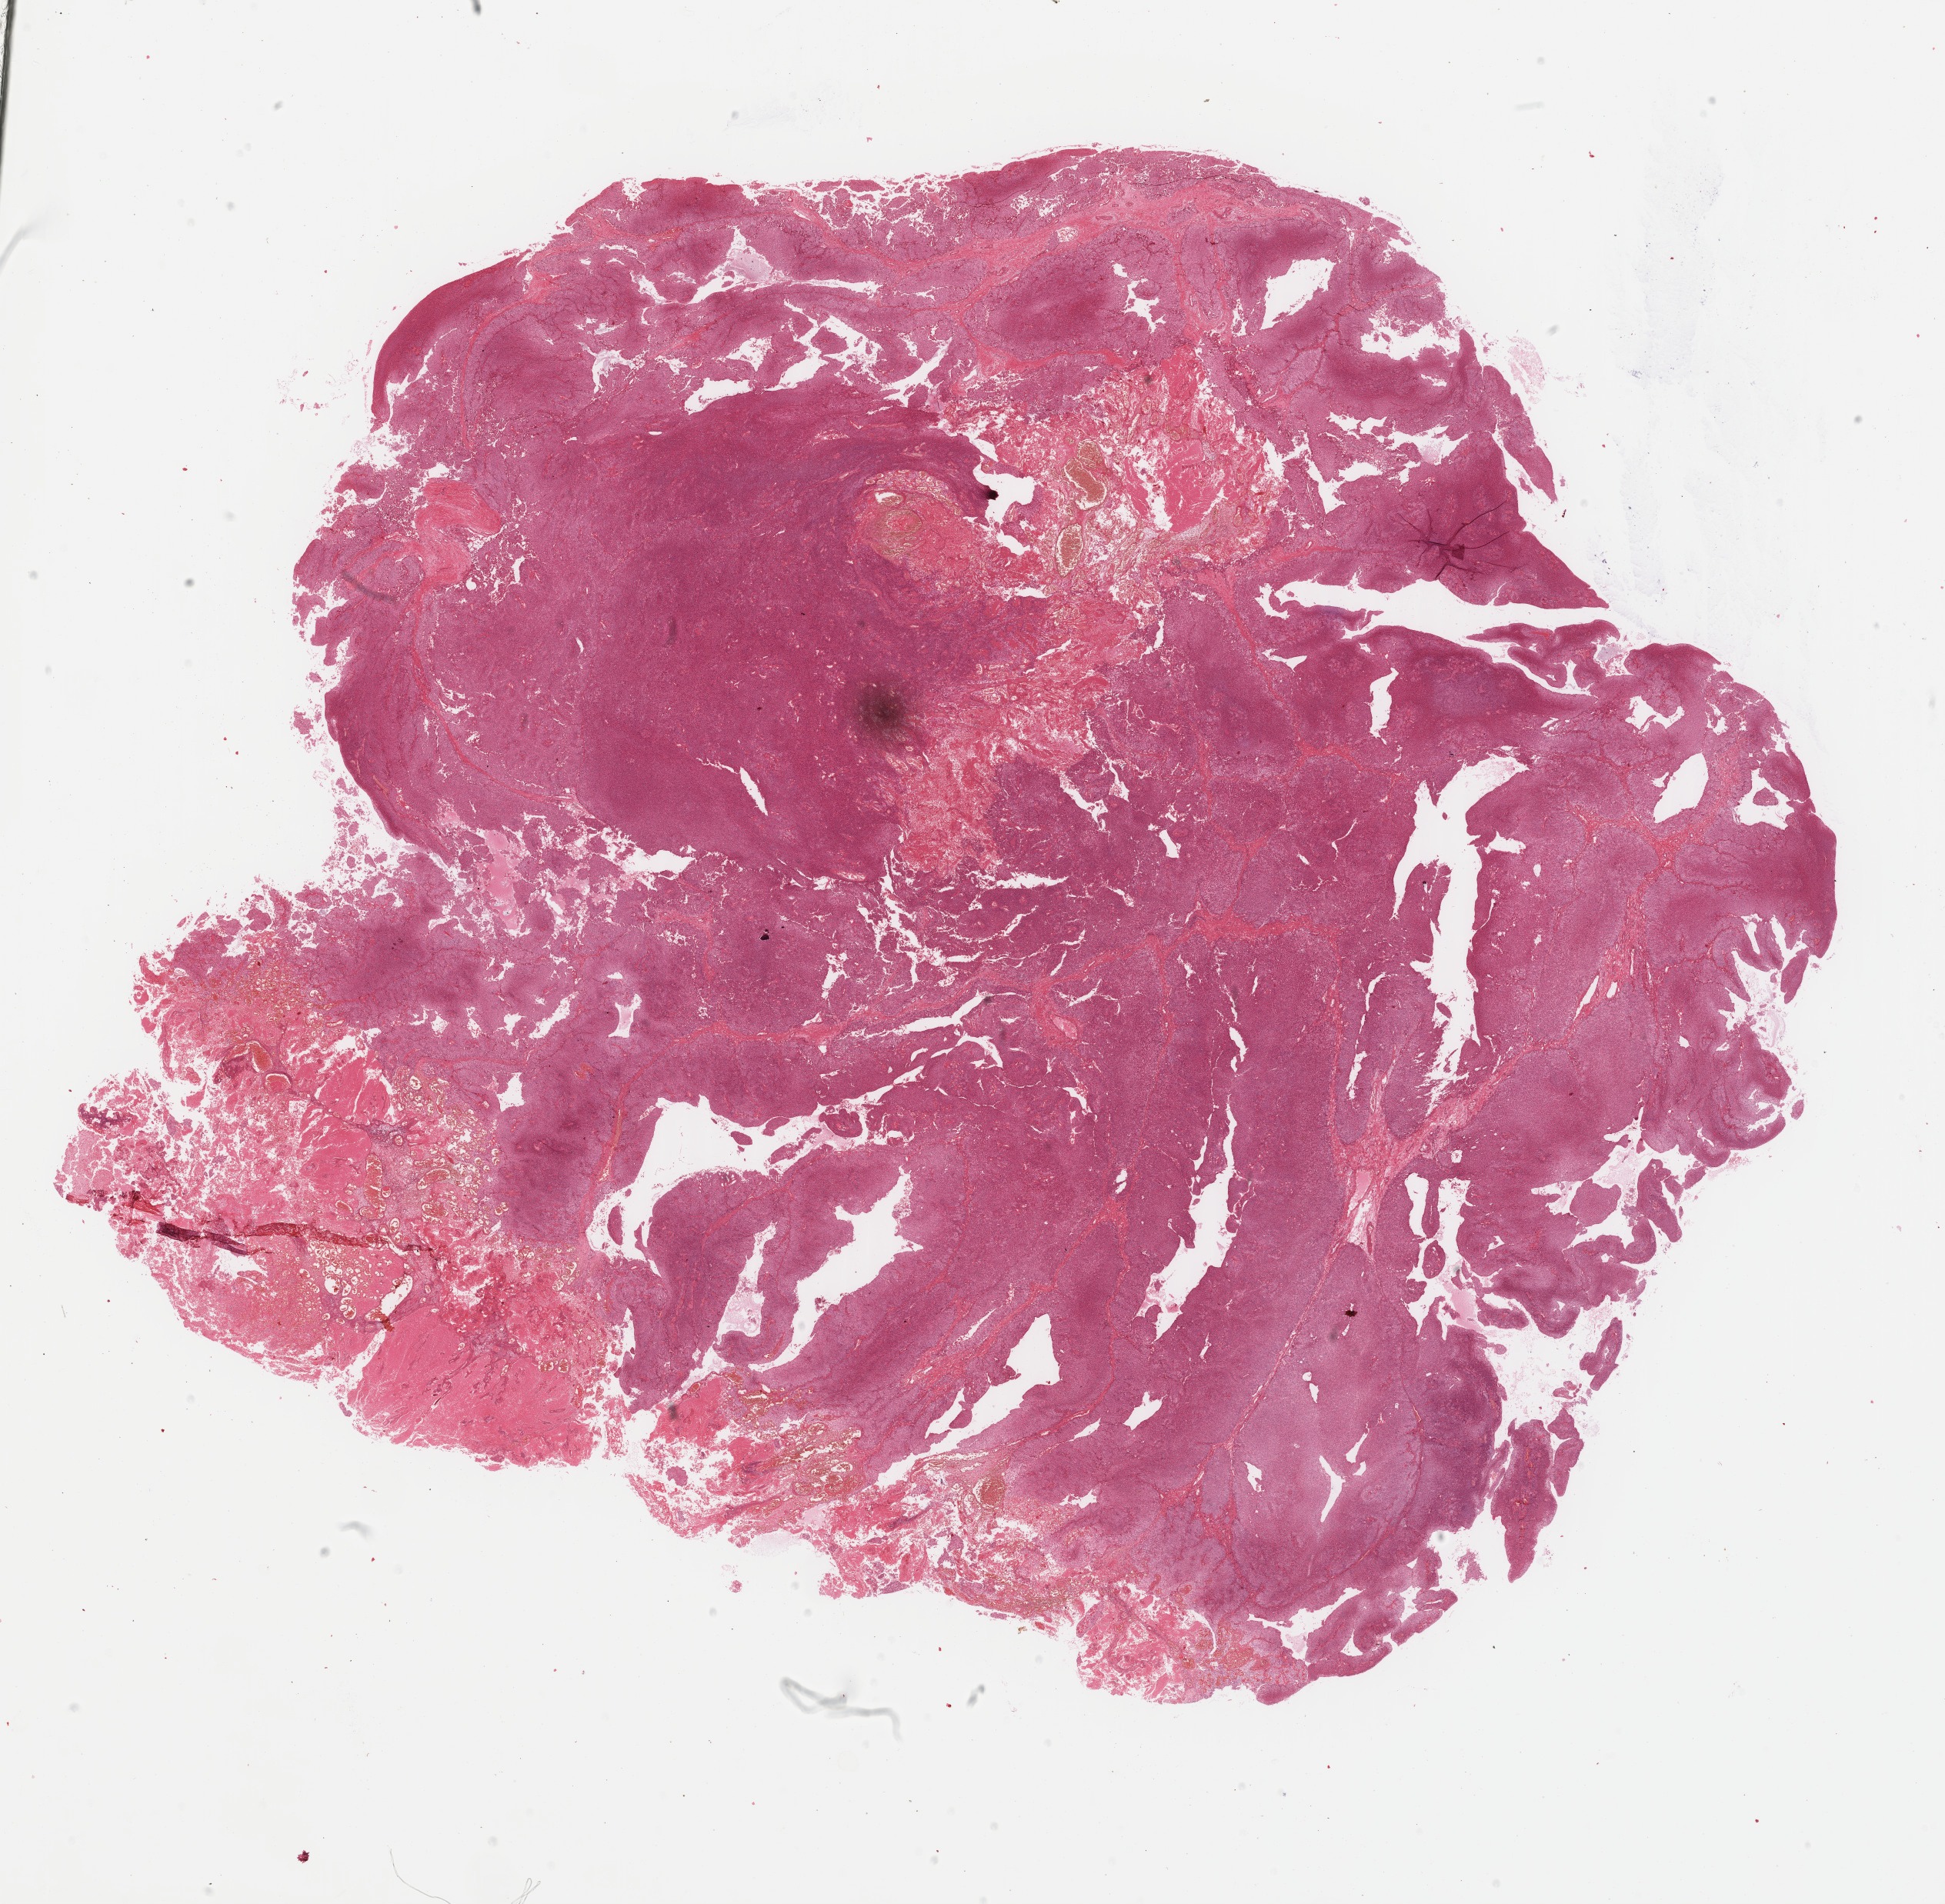
Digitized Hematoxylin and eosin (H&E) stained tissue section (whole slide), a low-resolution overview of the entire scanned area, about 20.1 x 19.6 mm; formalin-fixed paraffin-embedded (FFPE) diagnostic section; sample: primary tumour, bladder. Male patient; age at initial diagnosis 42 years.
Diagnosis: Papillary transitional cell carcinoma.